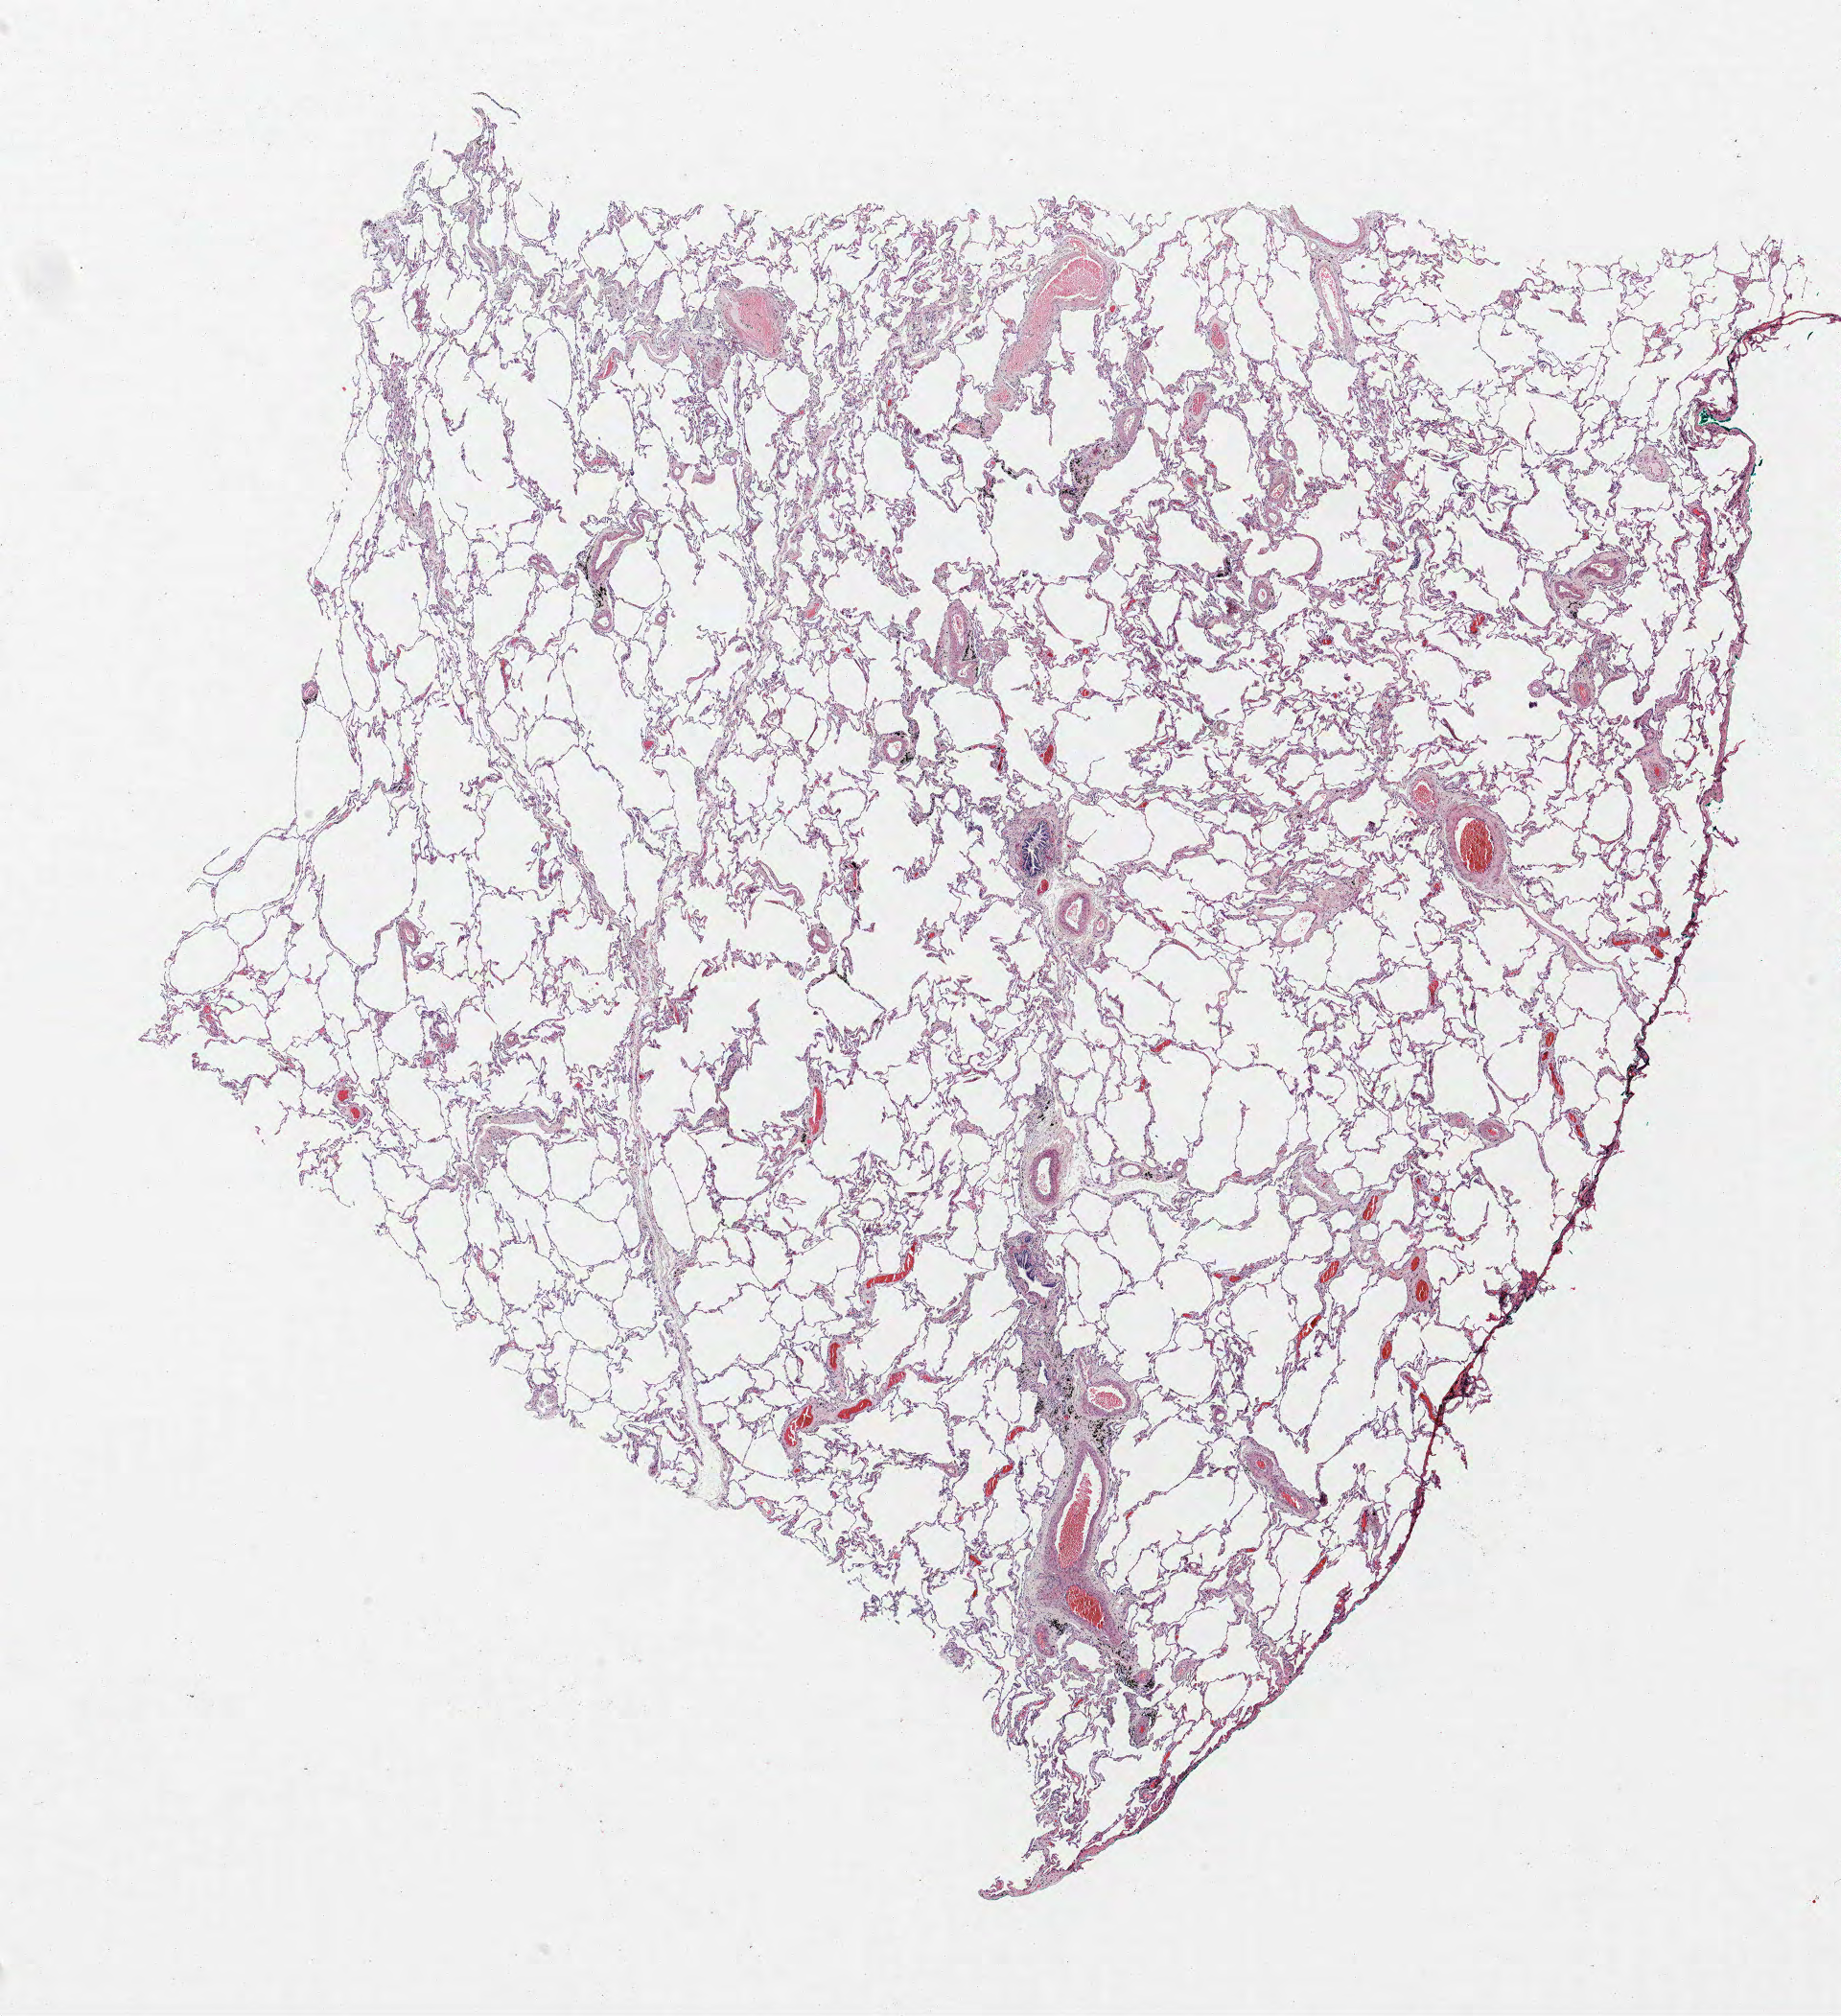
Whole-slide histology image, H&E — whole scanned area (about 15.4 x 16.8 mm, from a 40x scan) shown as a low-resolution overview, formalin-fixed paraffin-embedded (FFPE) section, lung tissue. Male, age 68 at enrolment. Former smoker at enrolment. Grade: poorly differentiated (G3).
Stage (AJCC 6th edition): IIB. Tumour size (pathology): 35 mm. ICD-O-3 topography: upper lobe of lung (C34.1). Primary tumour location (clinical record): left upper lobe. Participant's lung-cancer diagnosis: Squamous cell carcinoma, NOS (ICD-O-3 8070/3).